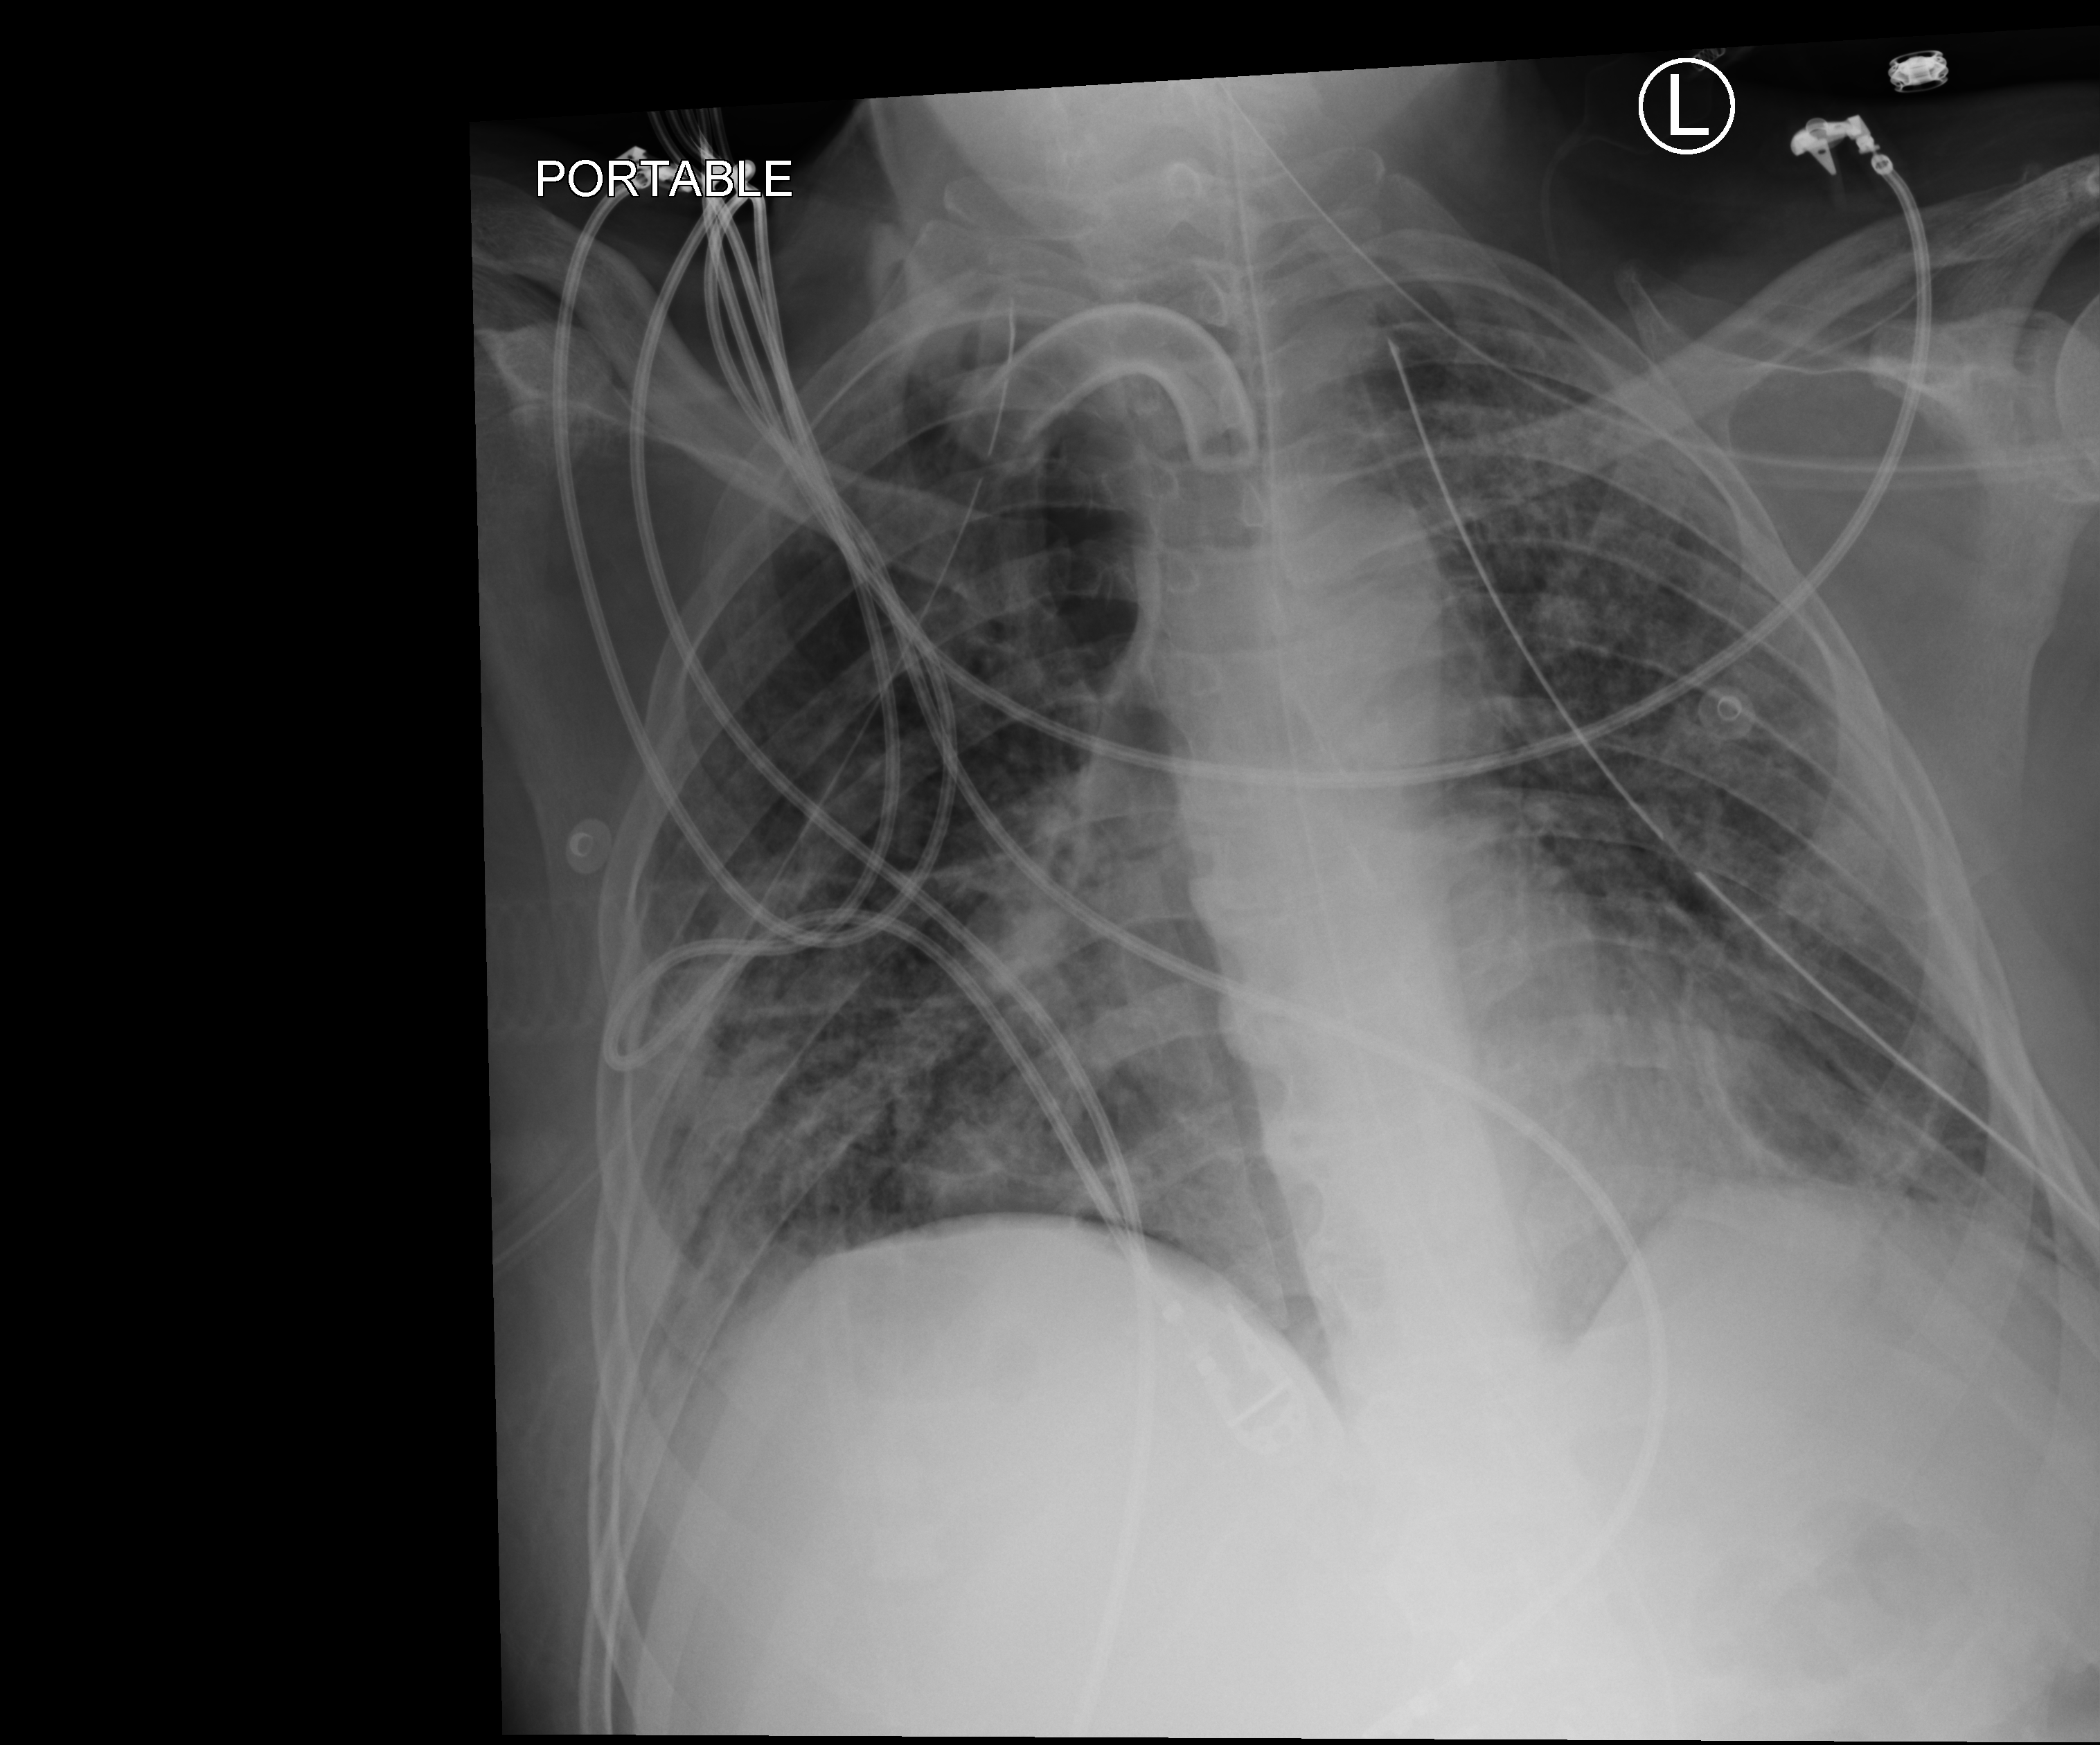
Bedside chest radiograph (computed radiography). Patient hospitalised with COVID-19; male, aged 18–59 years.
From the hospital-stay record, not from the radiograph (when in the stay this image was taken is not recorded): mechanically ventilated during this hospital stay: yes; chronic kidney disease (admission record): no; admitted to intensive care during this hospital stay: yes.